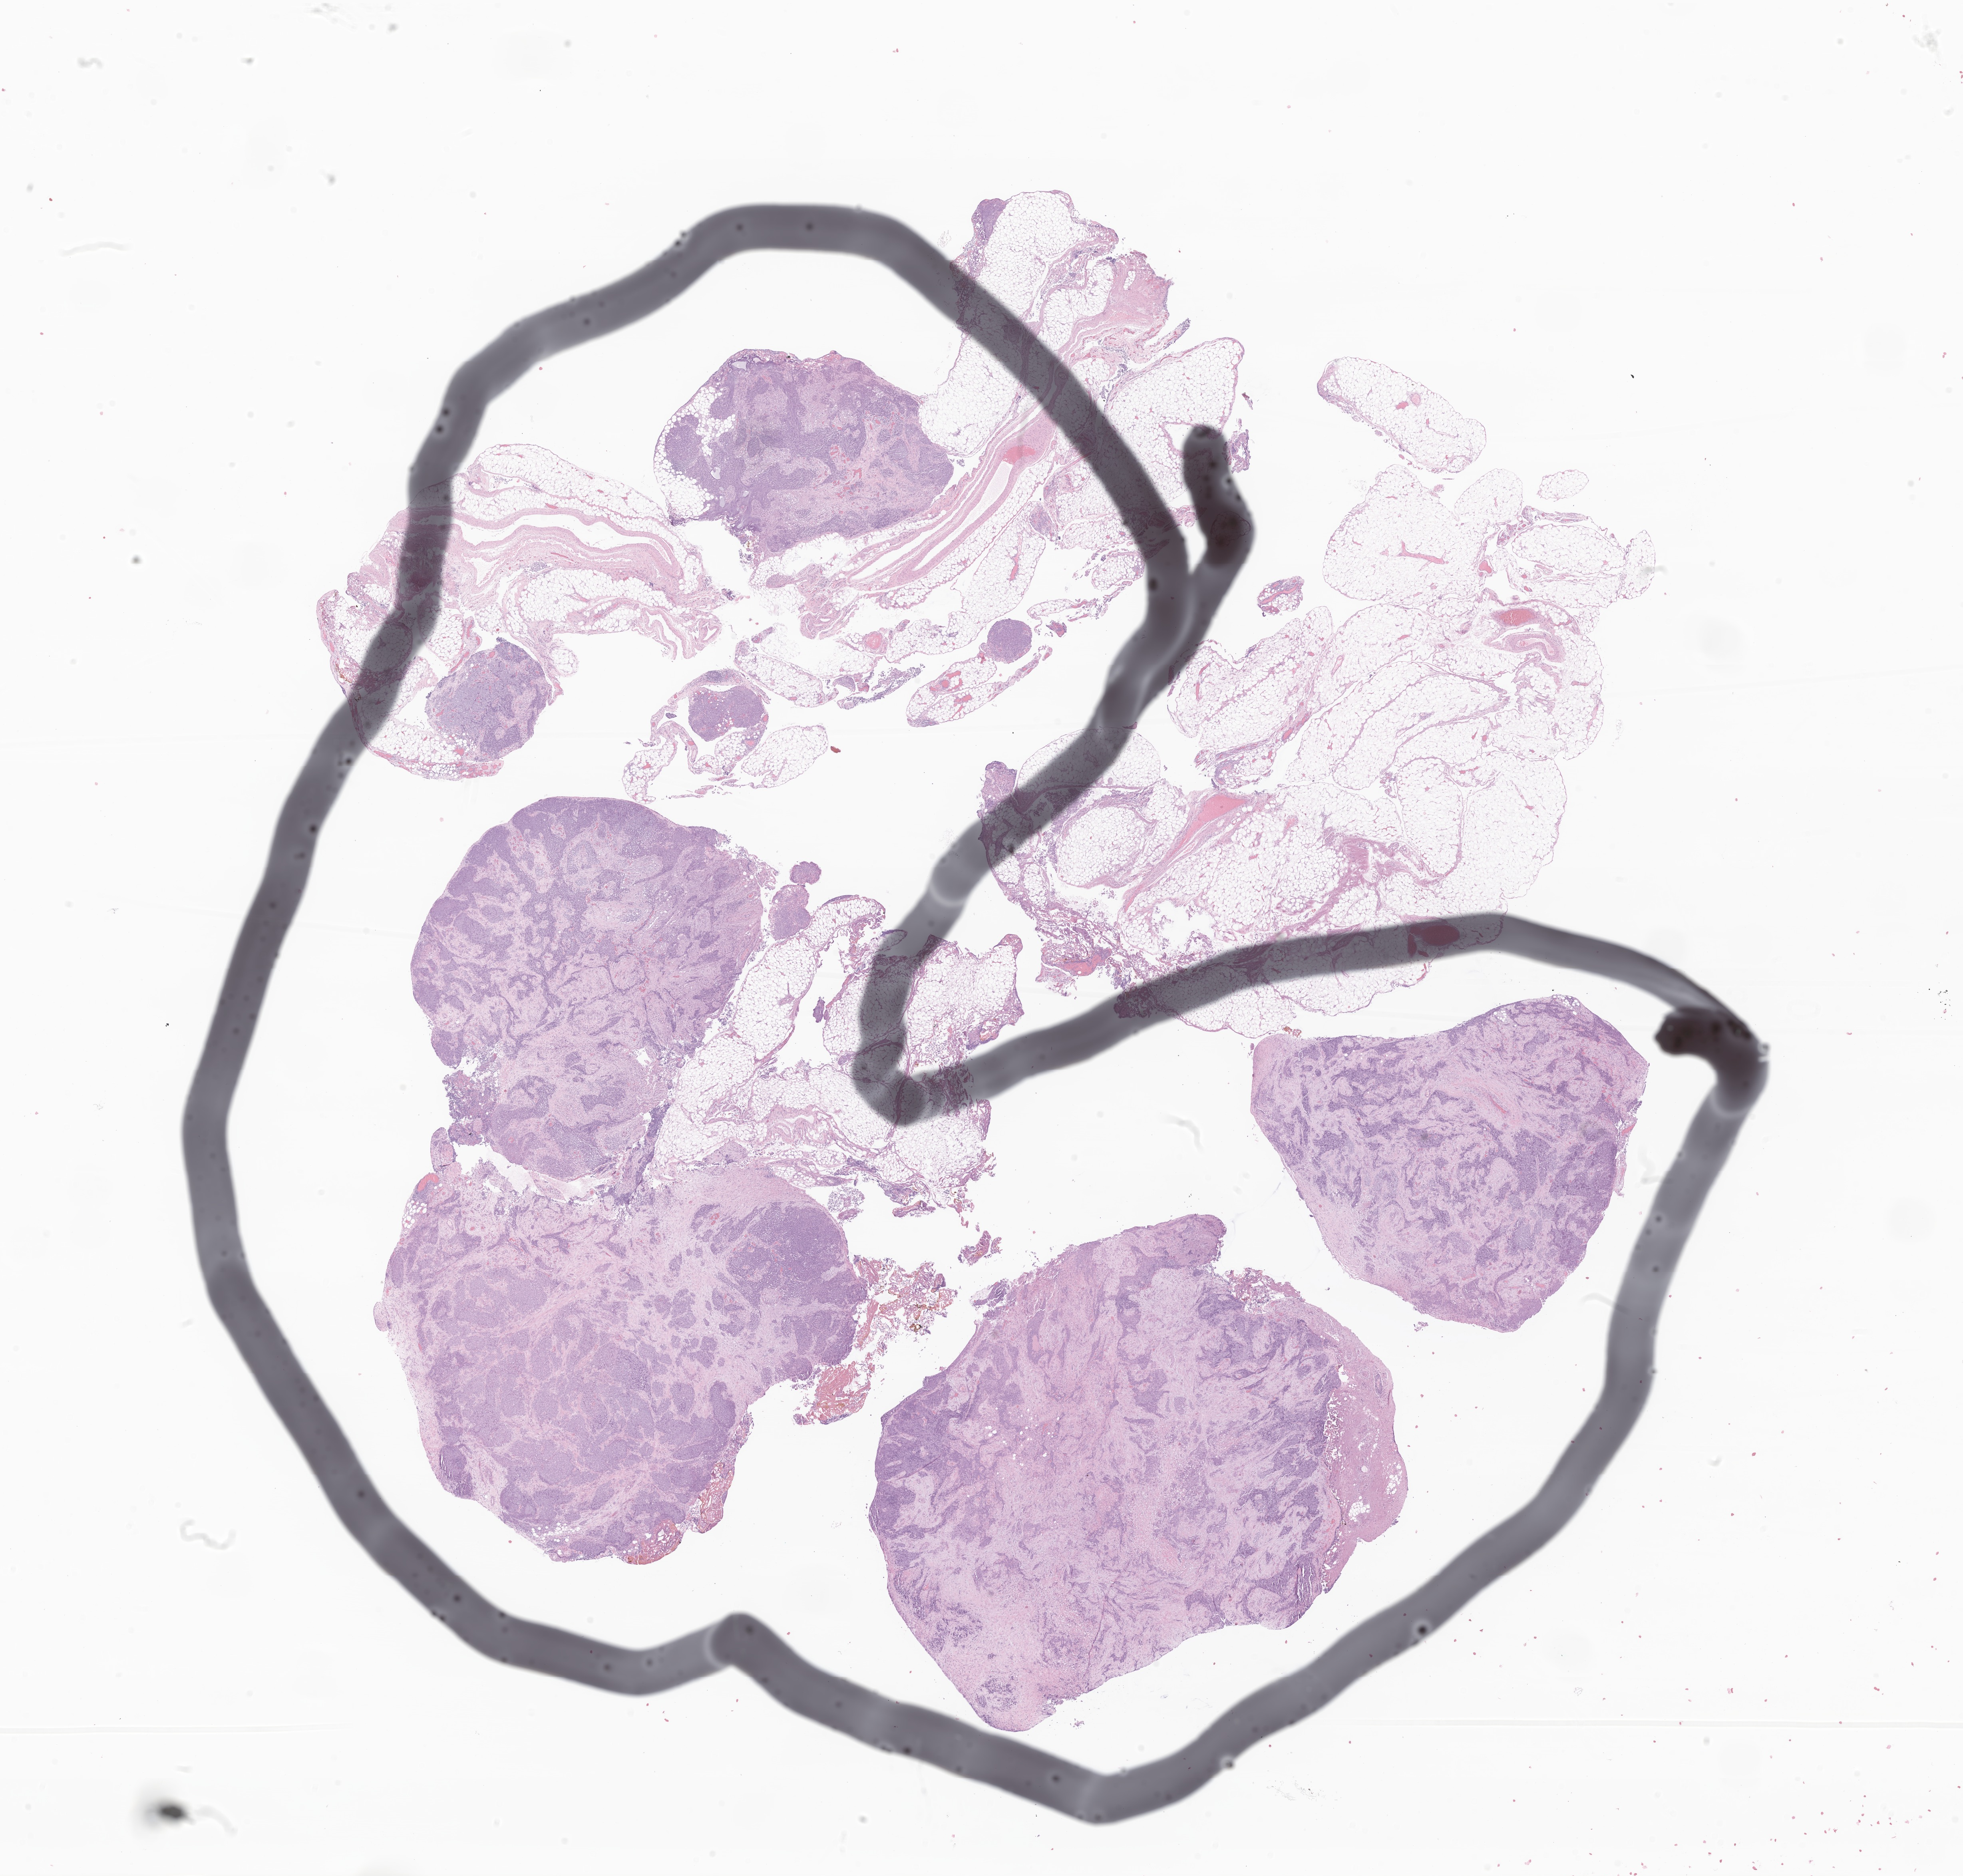
Digitized haematoxylin and eosin-stained section of tumor tissue from the abdomen, low-resolution overview of the scanned area, about 20.7 x 19.8 mm. Formalin-fixed, paraffin-embedded (FFPE) tissue. Female patient, age 200 months (16 years 8 months).
Recorded diagnosis: Ewing sarcoma.